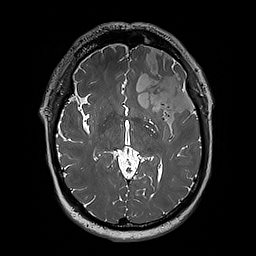
Brain MRI from a brain-tumour surgery series, one axial slice; 1 mm slice thickness; 256 × 256 image matrix, field of view 250 × 250 mm. Case-level facts recorded for this patient, not image findings: histopathology: Oligodendroglioma; WHO grade: 3; IDH mutation: yes.
Annotated regions visible in this slice (outlined manually by an expert reader):
- tumour: box from (x=124, y=49) to (x=197, y=124) px